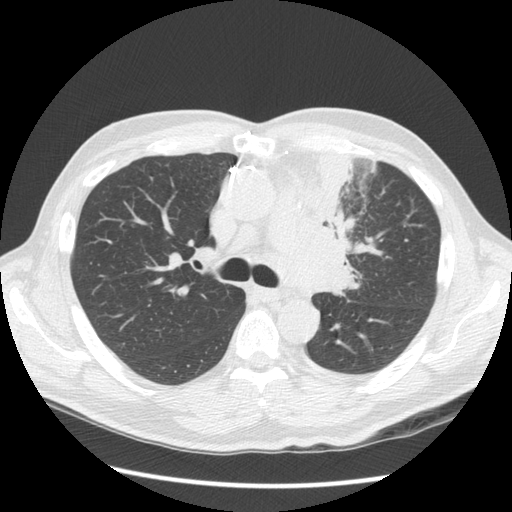
Low-dose screening chest CT, one axial slice; slice 91 of 136 in the series (ordered by position); 120 kVp; lung window (W 1500 / L -600 HU); 512 × 512 image matrix.
Annotated regions visible in this slice (manually delineated by an expert):
- lesion 1 (tumor, upper lobe of left lung): bounding box [x1, y1, x2, y2] px = [277, 151, 362, 296]